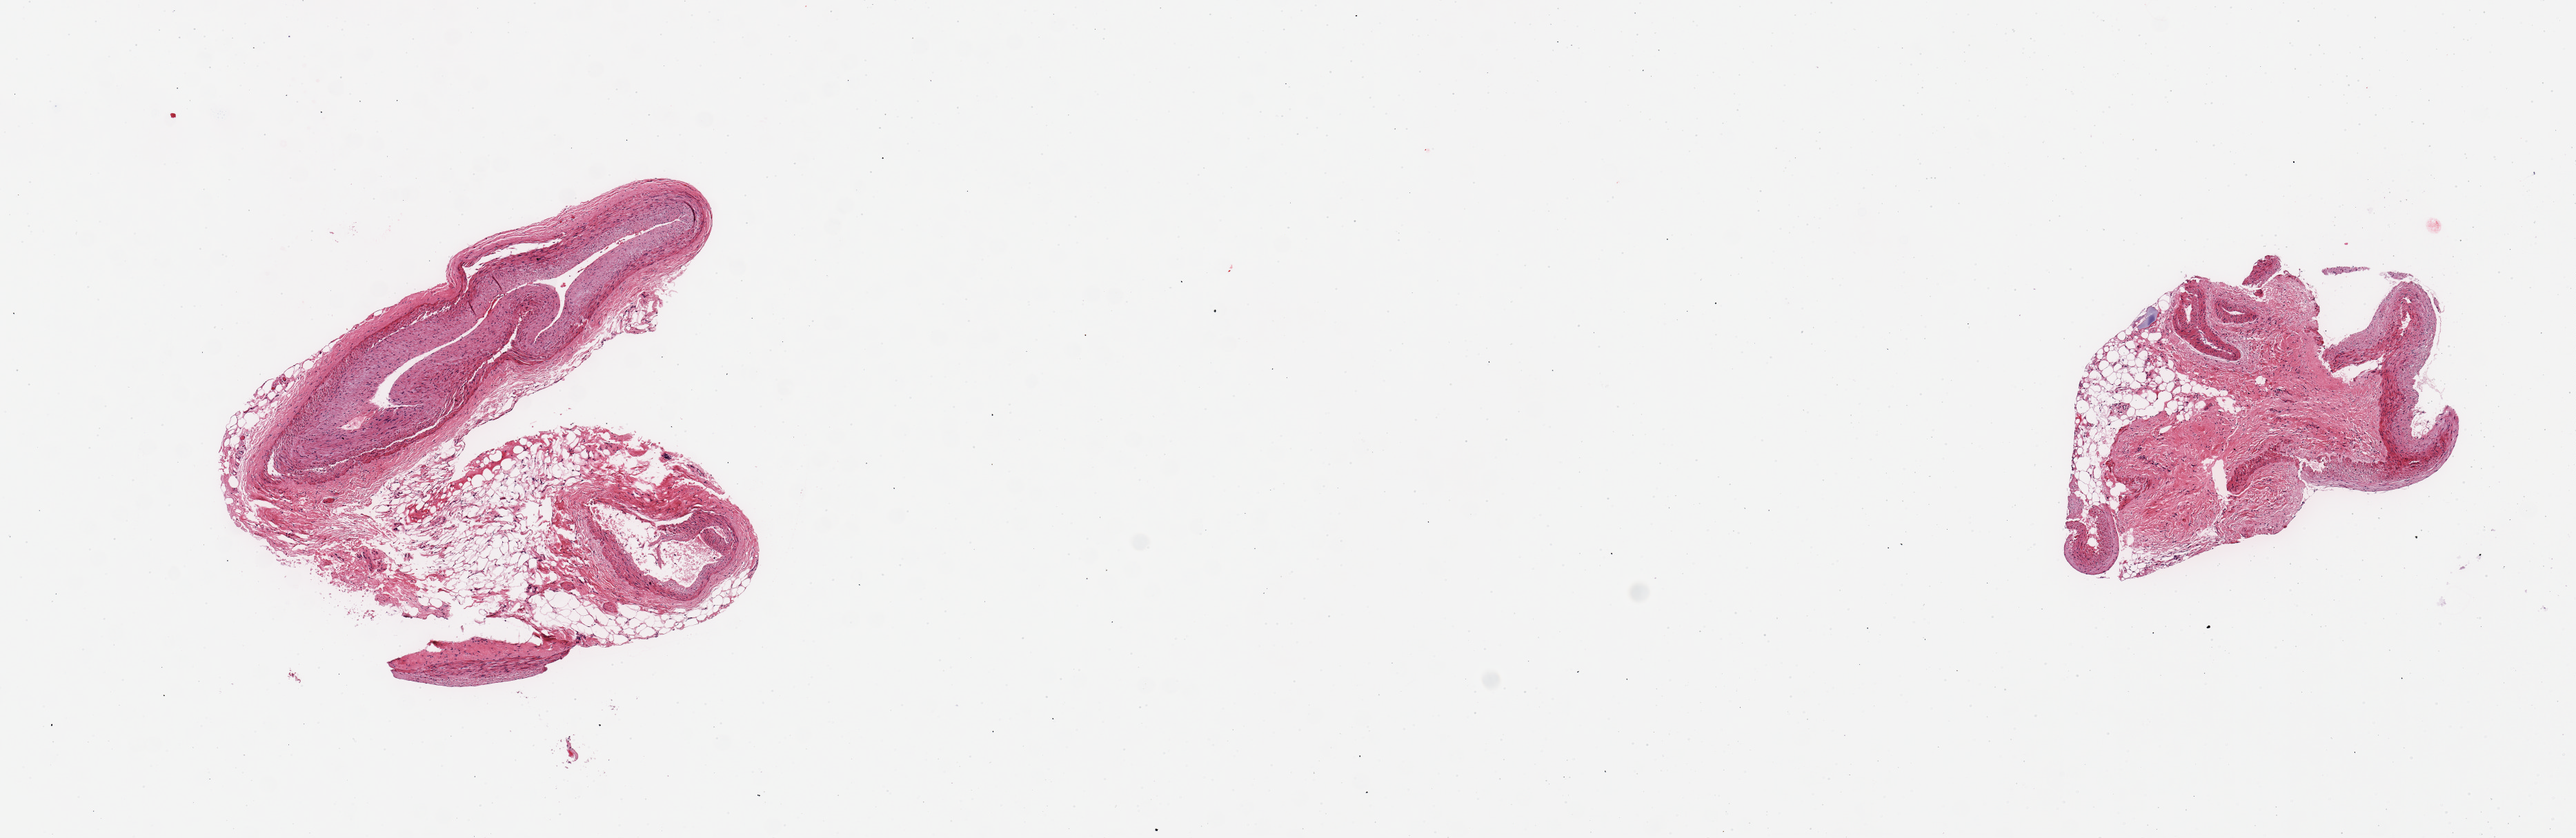
H&E whole-slide image, whole scanned area (about 14.8 x 4.8 mm) shown as a low-resolution overview. PAXgene-fixed paraffin-embedded (PFPE) section. Target tissue: coronary artery. Tissue donor sample. Male donor.
Pathologist's review note for this sample: 2 pieces, less than 50% vessel, mainly accessory twigs, fat, fibrous tissue.